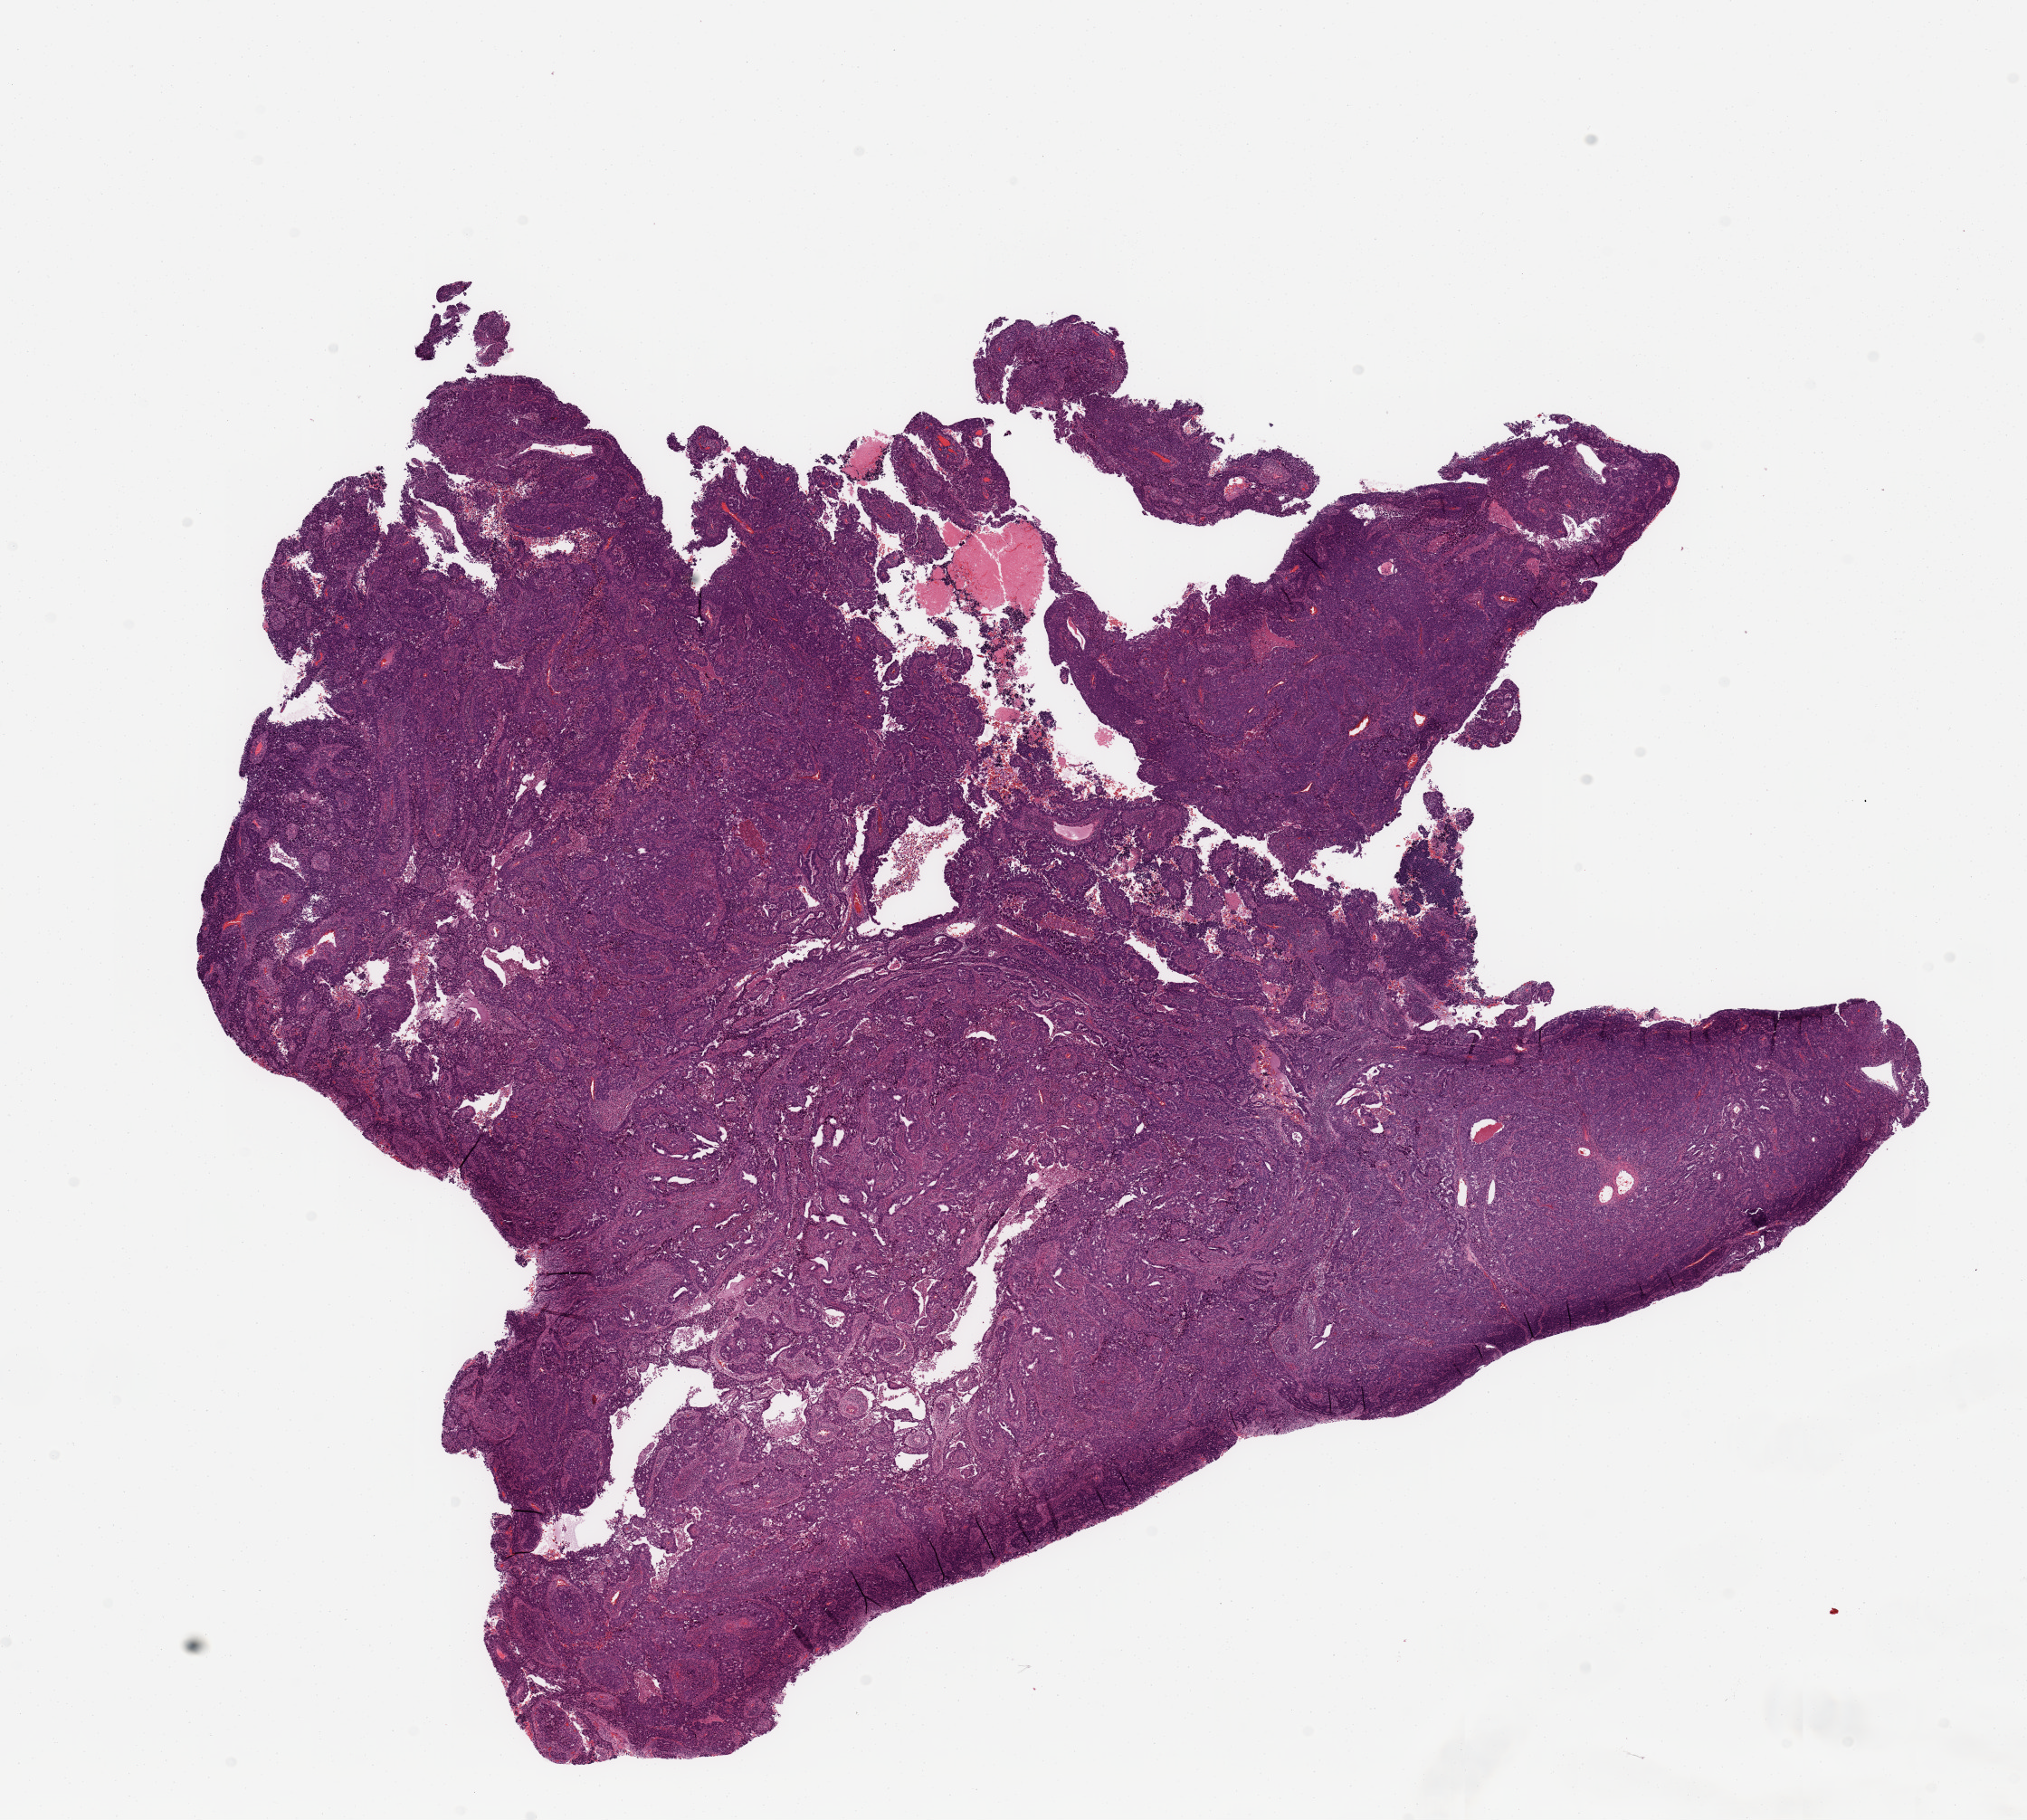
Whole-slide histology image, H&E-stained — whole scanned area (about 17.7 x 15.9 mm) shown as a low-resolution overview; tumour tissue sample, sampled site: uterus. Female patient, aged 90 or older. Pathologist review of this section (percent, as recorded): tumour nuclei 80%, necrosis 5%.
Diagnosis: Endometrioid adenocarcinoma, NOS.